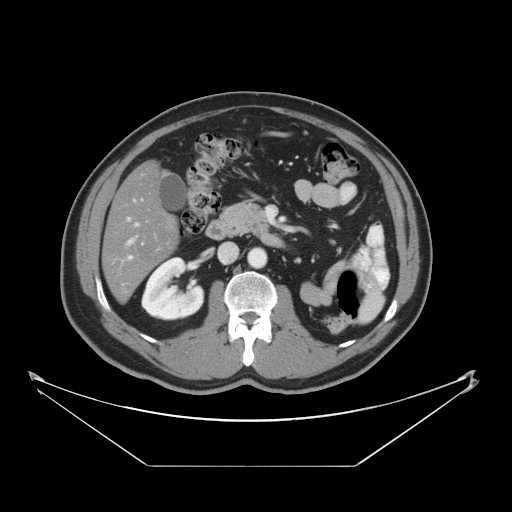
Contrast-enhanced abdominal CT, one axial slice; slice 18 of 46 in the series (ordered by position); 120 kVp; intravenous contrast given; soft-tissue window (W 400 / L 40 HU); 512 × 512 image matrix. Male patient, age 57 years. Case-level facts recorded for this patient, not image findings: diagnosis: colorectal cancer liver metastases, imaged before liver resection; multiple liver metastases: no; largest metastasis: 3.3 cm; disease in both lobes: no.
Outlined on this slice (expert manual segmentation):
- hepatic veins: bounding box <128,218,138,244> (left, top, right, bottom; pixels)
- liver: <104,163,178,301>
- planned liver remnant (the part of the liver to remain after resection): <104,163,177,301>
- portal vein (with intrahepatic branches): <129,256,132,259>